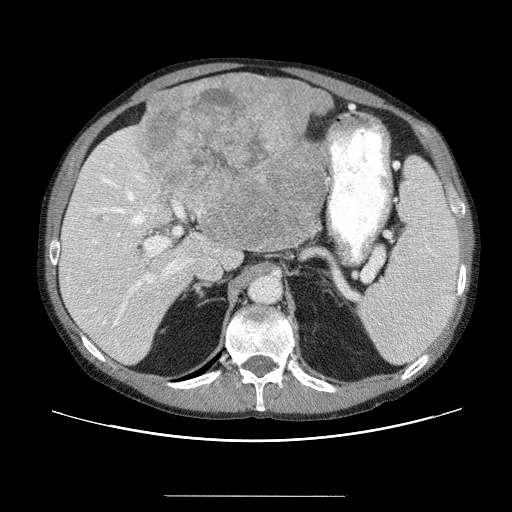
Contrast-enhanced abdominal CT (liver protocol), one axial slice. Position 30 of 69 along the scan axis. Reconstruction kernel STANDARD. 120 kVp. Soft-tissue window (W 400 / L 40 HU). 2.5 mm slice thickness. 512 × 512 image matrix, field of view 380 × 380 mm. Case-level facts recorded for this patient, not image findings: diagnosis: hepatocellular carcinoma (patient treated with transarterial chemoembolisation; whether this scan precedes or follows treatment is not stated here); TNM stage (as recorded): Stage-IVB; Child-Pugh class: B.
Outlined on this slice (semi-automatically segmented with operator editing):
- liver parenchyma outside the tumour (the mass and vessels are separate outlines, so this box may not span the whole liver): bounding box (x1, y1, x2, y2) in pixels: (58, 103, 244, 362)
- mass: (134, 74, 334, 253)
- liver vessels: (69, 150, 193, 341)